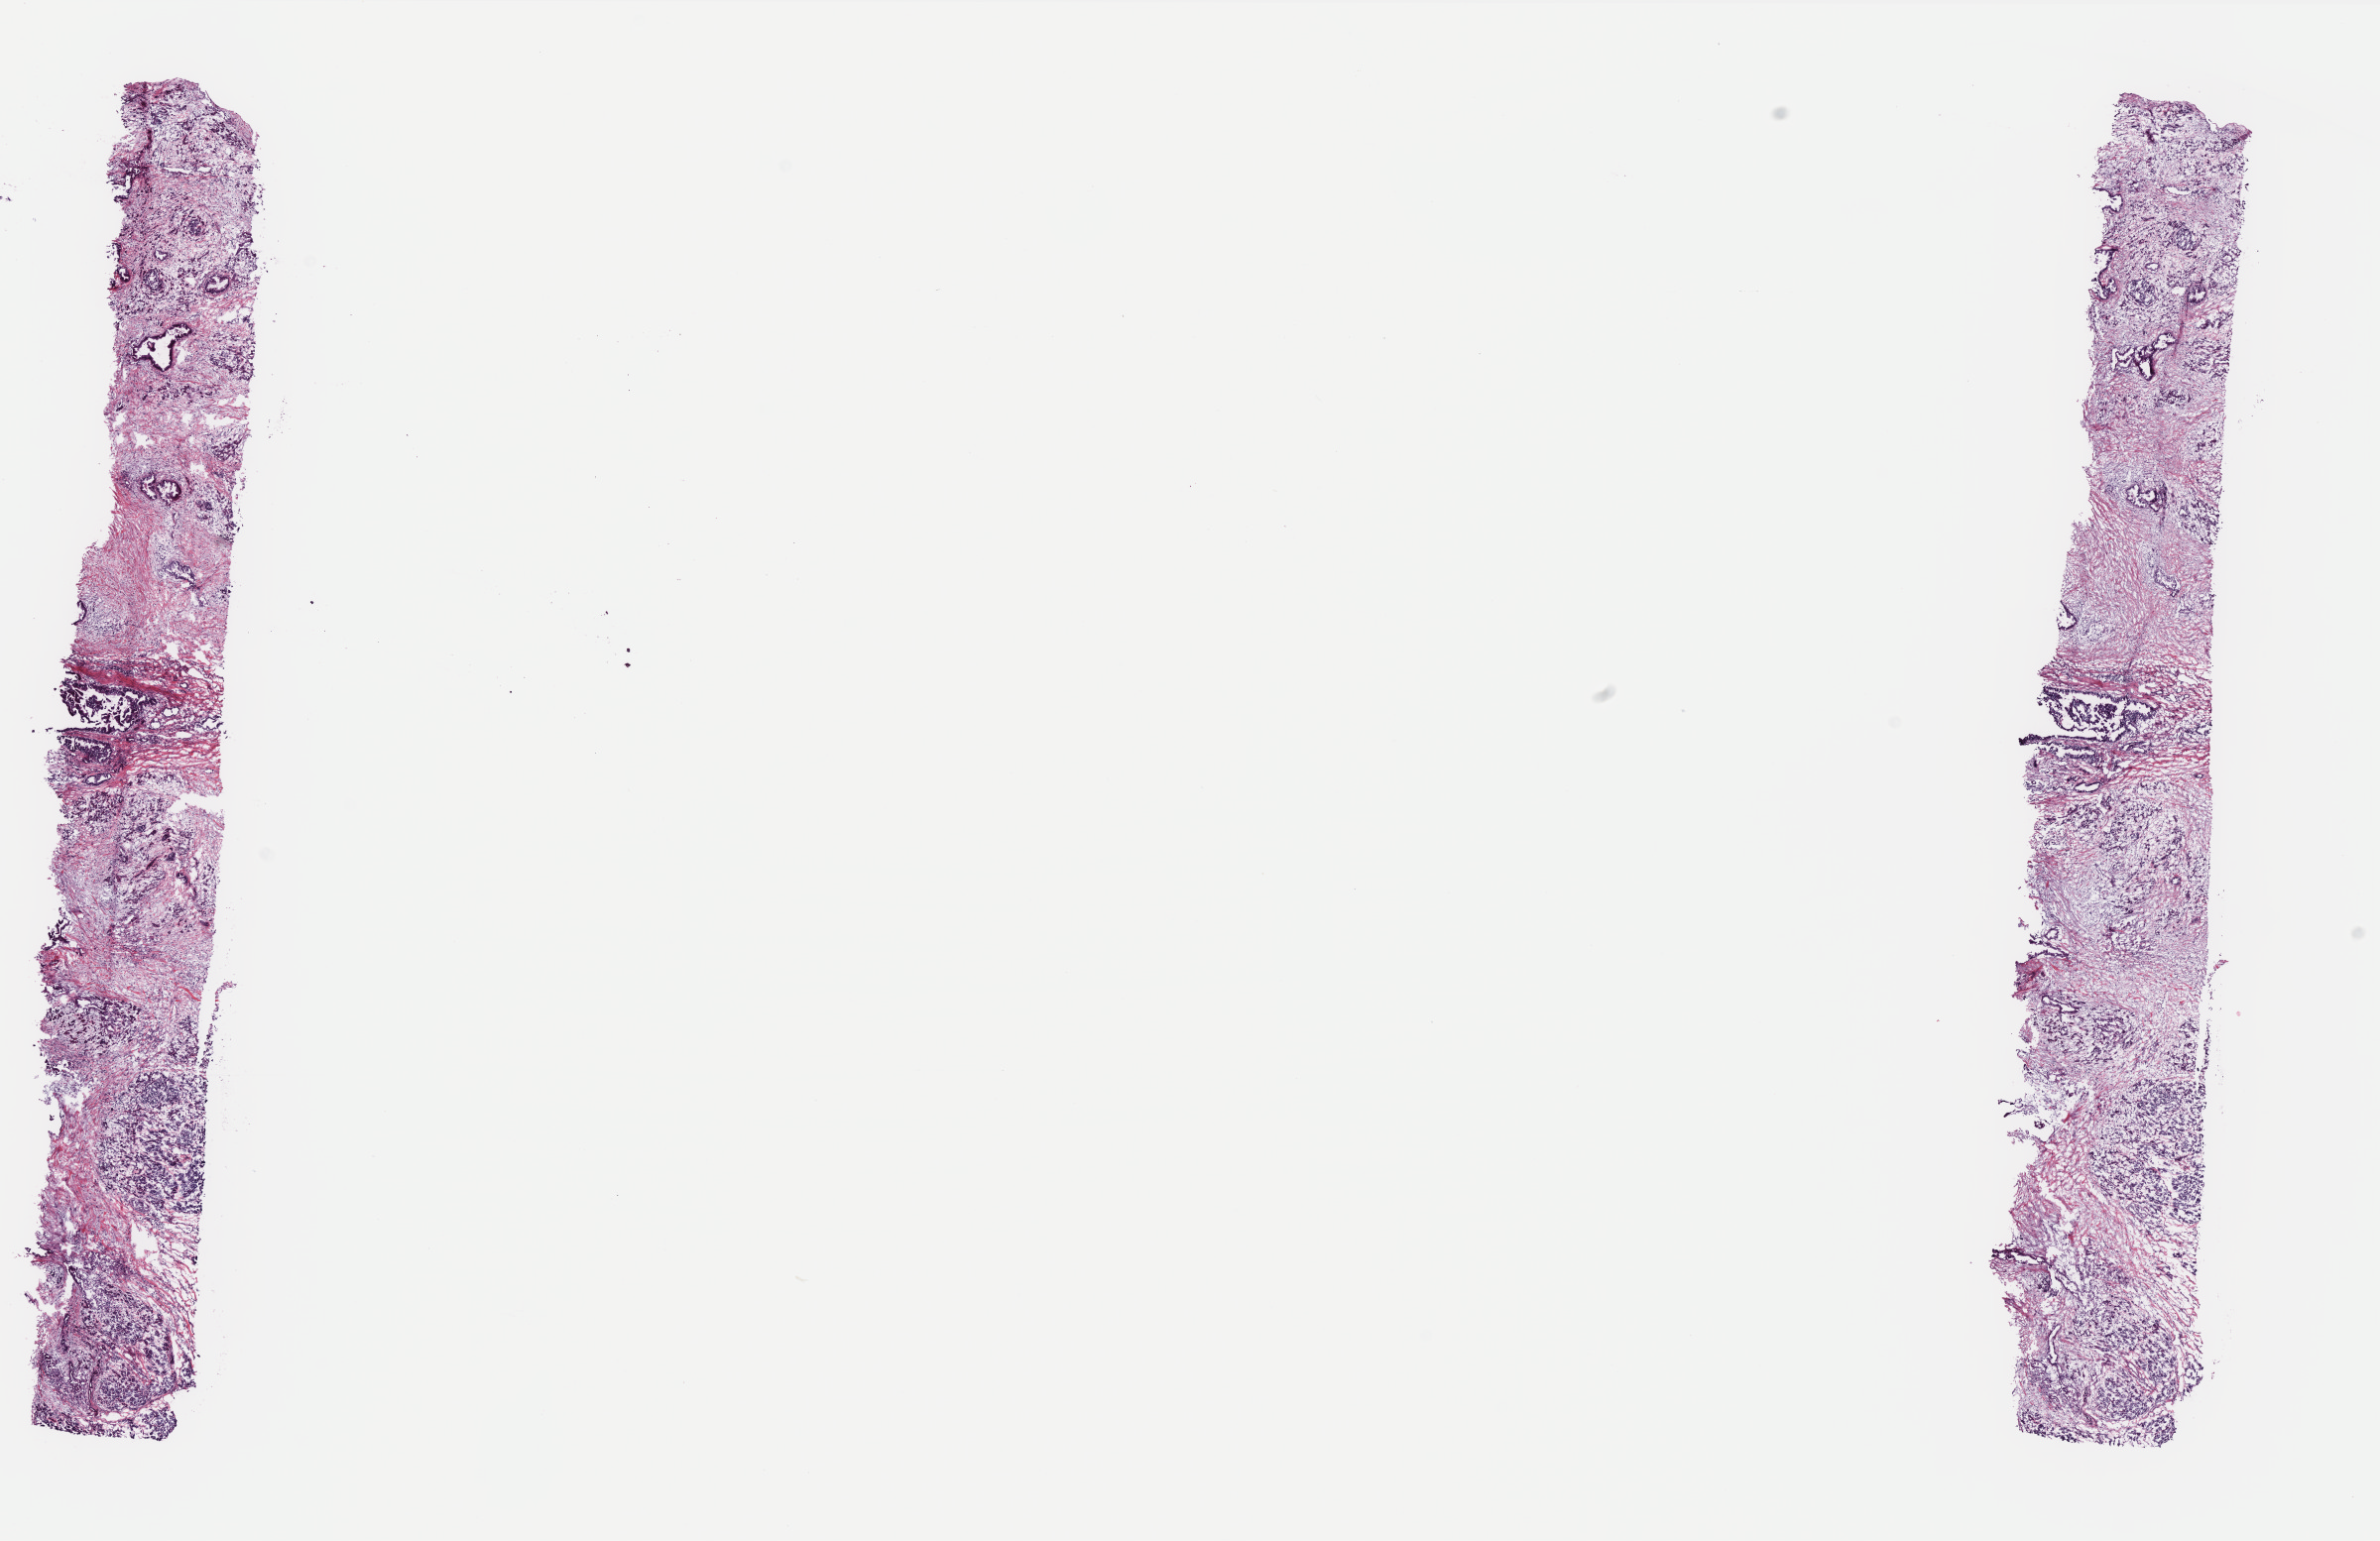
Digitized Hematoxylin and eosin (H&E) stained tissue section (whole slide) — a low-resolution overview of the entire scanned area, about 19.2 x 12.5 mm (slide scanned at 40x), frozen section from the top of the tissue portion, primary tumour sample from the pancreas. Patient: female, age at initial diagnosis 54 years. Histologic grade: G1 (well differentiated). Composition of this section per pathologist review: tumour cells 20%, tumour nuclei 30%, normal cells 40%, stromal cells 40%, necrosis 0%. Infiltration values recorded for this section: lymphocyte infiltration 8%, monocyte infiltration 4%, neutrophil infiltration 0%.
• diagnosis: Infiltrating duct carcinoma, NOS (head of pancreas)
• AJCC pathologic stage: IIB
• lymph nodes positive (case pathology): 2 of 21 examined